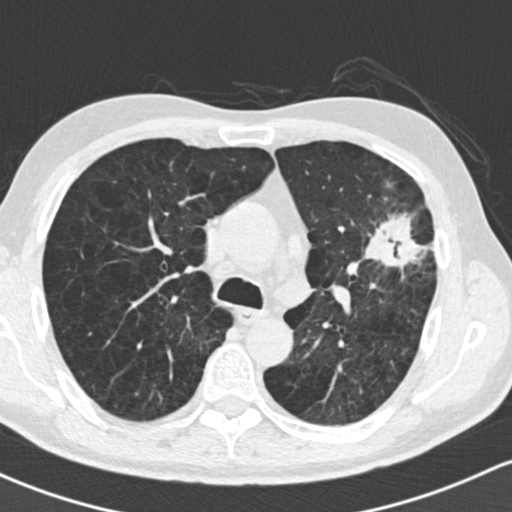
Low-dose screening chest CT, axial slice. Baseline annual screen. Lung window (W 1500 / L -600 HU). 2 mm slice thickness. Slice 60 of 162 in the series. Male participant, aged 61 years at enrolment.
• Lesion marked by an expert reader, box from (x=355, y=186) to (x=452, y=293) px.
• The exam's reader record, not a measurement of the box and not confirmed to be the same lesion: non-calcified nodule or mass ≥4 mm, left upper lobe, 35 × 35 mm, spiculated (stellate) margins, soft tissue attenuation.
• Participant outcome: lung cancer diagnosed 19 days after this screen — adenocarcinoma, NOS, left upper lobe, well differentiated (G1), stage IIIA (AJCC 6th edition), 45 mm at pathology.